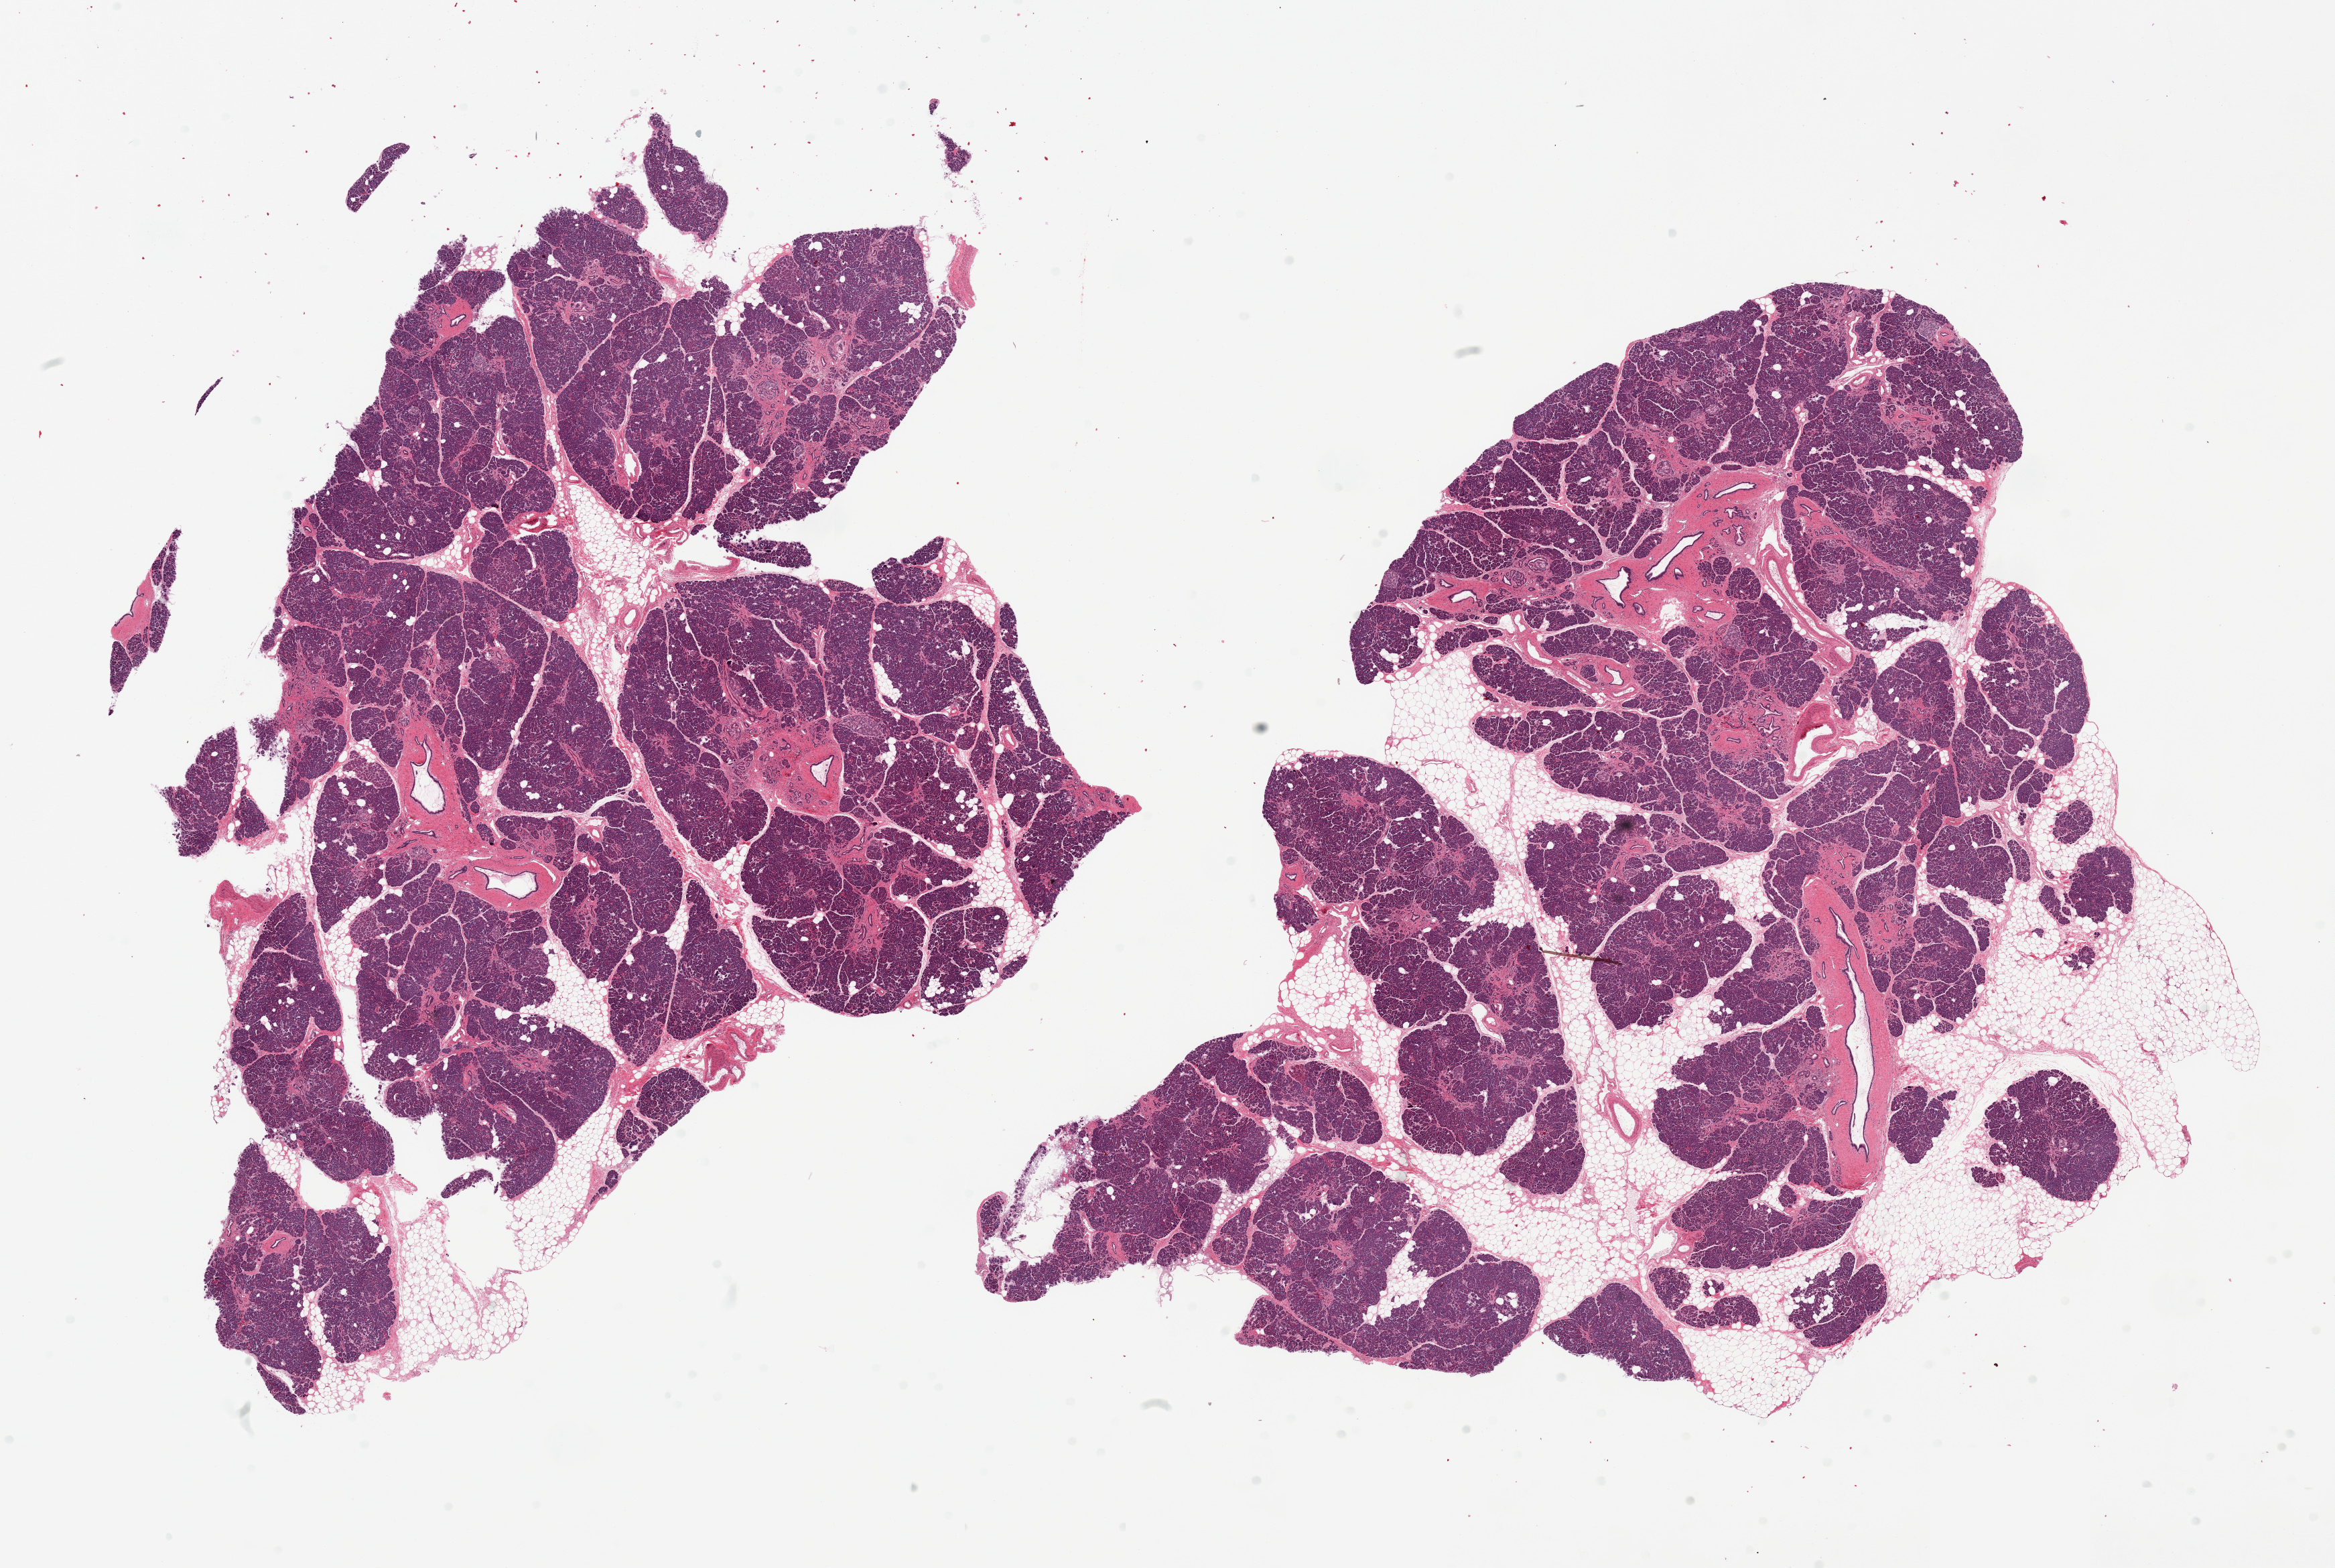
Digitized H&E-stained section, low-resolution overview of the scanned area, about 27.6 x 18.5 mm (acquisition: 20x scan); PAXgene-fixed, paraffin-embedded tissue; target tissue: pancreas; donor tissue sample. Donor: male.
Pathologist's review note for this sample: 2 pieces, includes 10-20% internal and attached adipose tissue, some atrophy and fibrosis, focal islets with amyloid-like material.